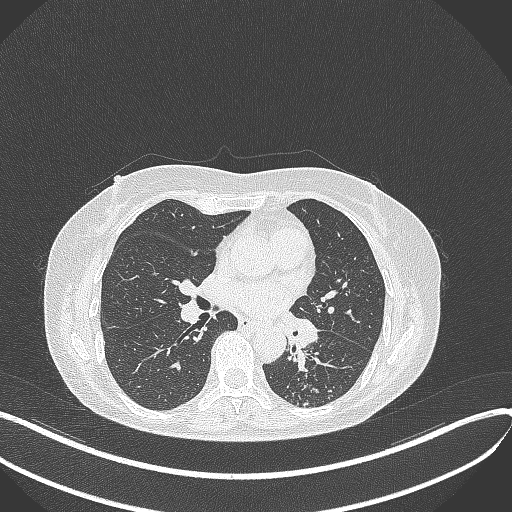
Chest CT, one axial slice. Position 212 of 429 along the scan axis. Lung window (W 1500 / L -600 HU). 1 mm slice thickness. 512 × 512 image matrix, field of view 400 × 400 mm. Patient: female, 63 years. Case-level facts recorded for this patient, not image findings: clinical TNM (as recorded): T1b N0 M0; histopathological grade: G2-3.
Annotated regions visible in this slice (rectangle marked by the reading radiologist):
- lung tumour (recorded histology: adenocarcinoma): box from (x=281, y=313) to (x=327, y=351) px